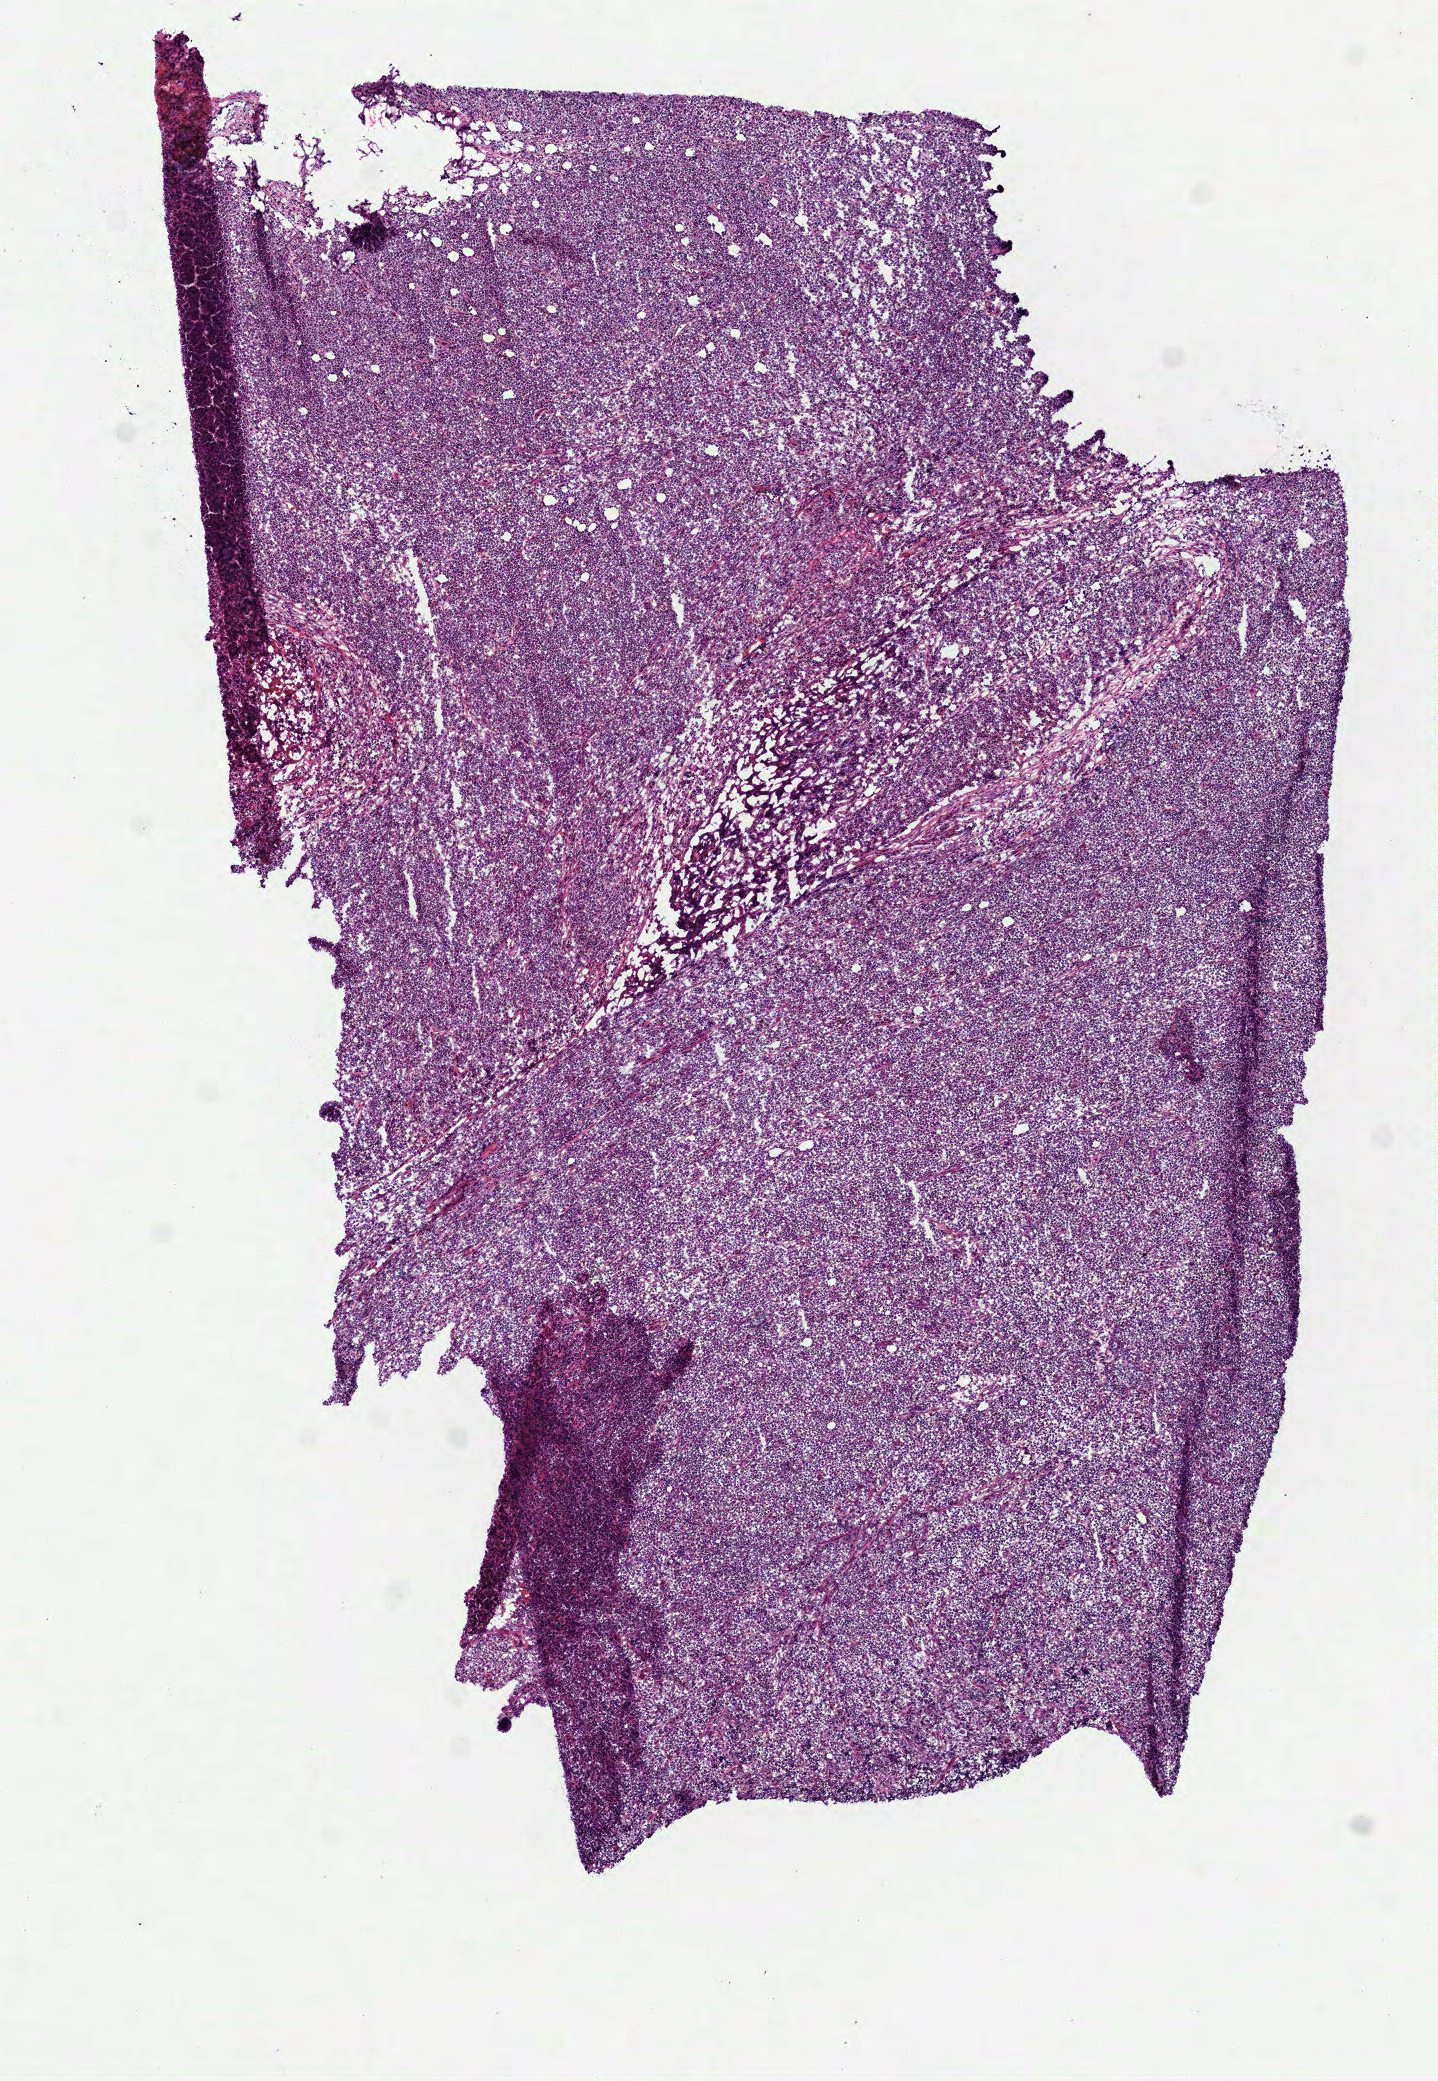
Digitized H&E-stained tissue section (whole slide) — shown as a low-resolution overview of the whole scanned area (about 5.8 x 8.4 mm, acquisition: 40x scan), frozen section from the top of the tissue portion, lymphoid tissue, primary tumour sample. Female, age 57 years at initial diagnosis. Slide review estimates, as recorded: tumour cells 100%, tumour nuclei 90%, normal cells 0%, stromal cells 0%, necrosis 0%. Inflammatory infiltration, as recorded: lymphocyte infiltration 9%, monocyte infiltration 0%, neutrophil infiltration 0%.
Diagnosis: Diffuse large B-cell lymphoma, NOS (lymph nodes of head, face and neck).